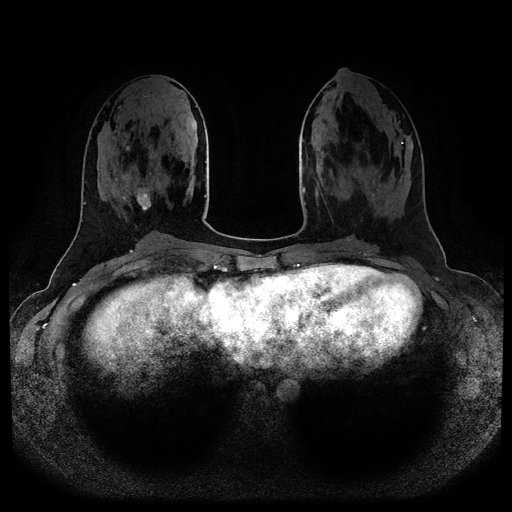
Breast MRI (dynamic contrast-enhanced, multi-phase), one axial slice; slice 40 of 116 in the series (ordered by position); dynamic contrast-enhanced series, time point 2 of 5 at this slice position (early post-contrast); 1.5 T; TE 2.6 ms, TR 5.2 ms; 512 × 512 image matrix, field of view 380 × 380 mm. Patient: female, 25 years.
Annotated regions visible in this slice (semi-automatically segmented with operator editing):
- breast lesion (labelled benign in the annotation): bounding box (x1, y1, x2, y2) in pixels: (136, 183, 152, 211)